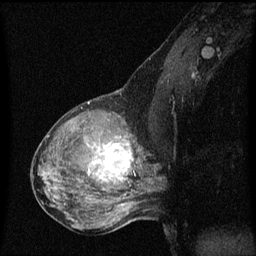
Breast MRI (dynamic contrast-enhanced), one sagittal slice. Position 33 of 60 along the scan axis. Dynamic contrast-enhanced series, image 2 of 3 at this slice position (ordered by acquisition). 1.5 T. TE 4.2 ms, TR 8 ms. 2 mm slice thickness. 256 × 256 image matrix, field of view 200 × 200 mm. Patient: female, 50 years.
Annotated regions visible in this slice (semi-automatically segmented with operator editing):
- analysis volume of interest (the breast-tissue region the enhancement analysis was run in; not a lesion): bounding box (x1, y1, x2, y2) in pixels: (91, 126, 141, 189)
- tumour enhancement mask (voxels above the 70 % enhancement threshold inside the analysis volume of interest): (92, 138, 134, 179)